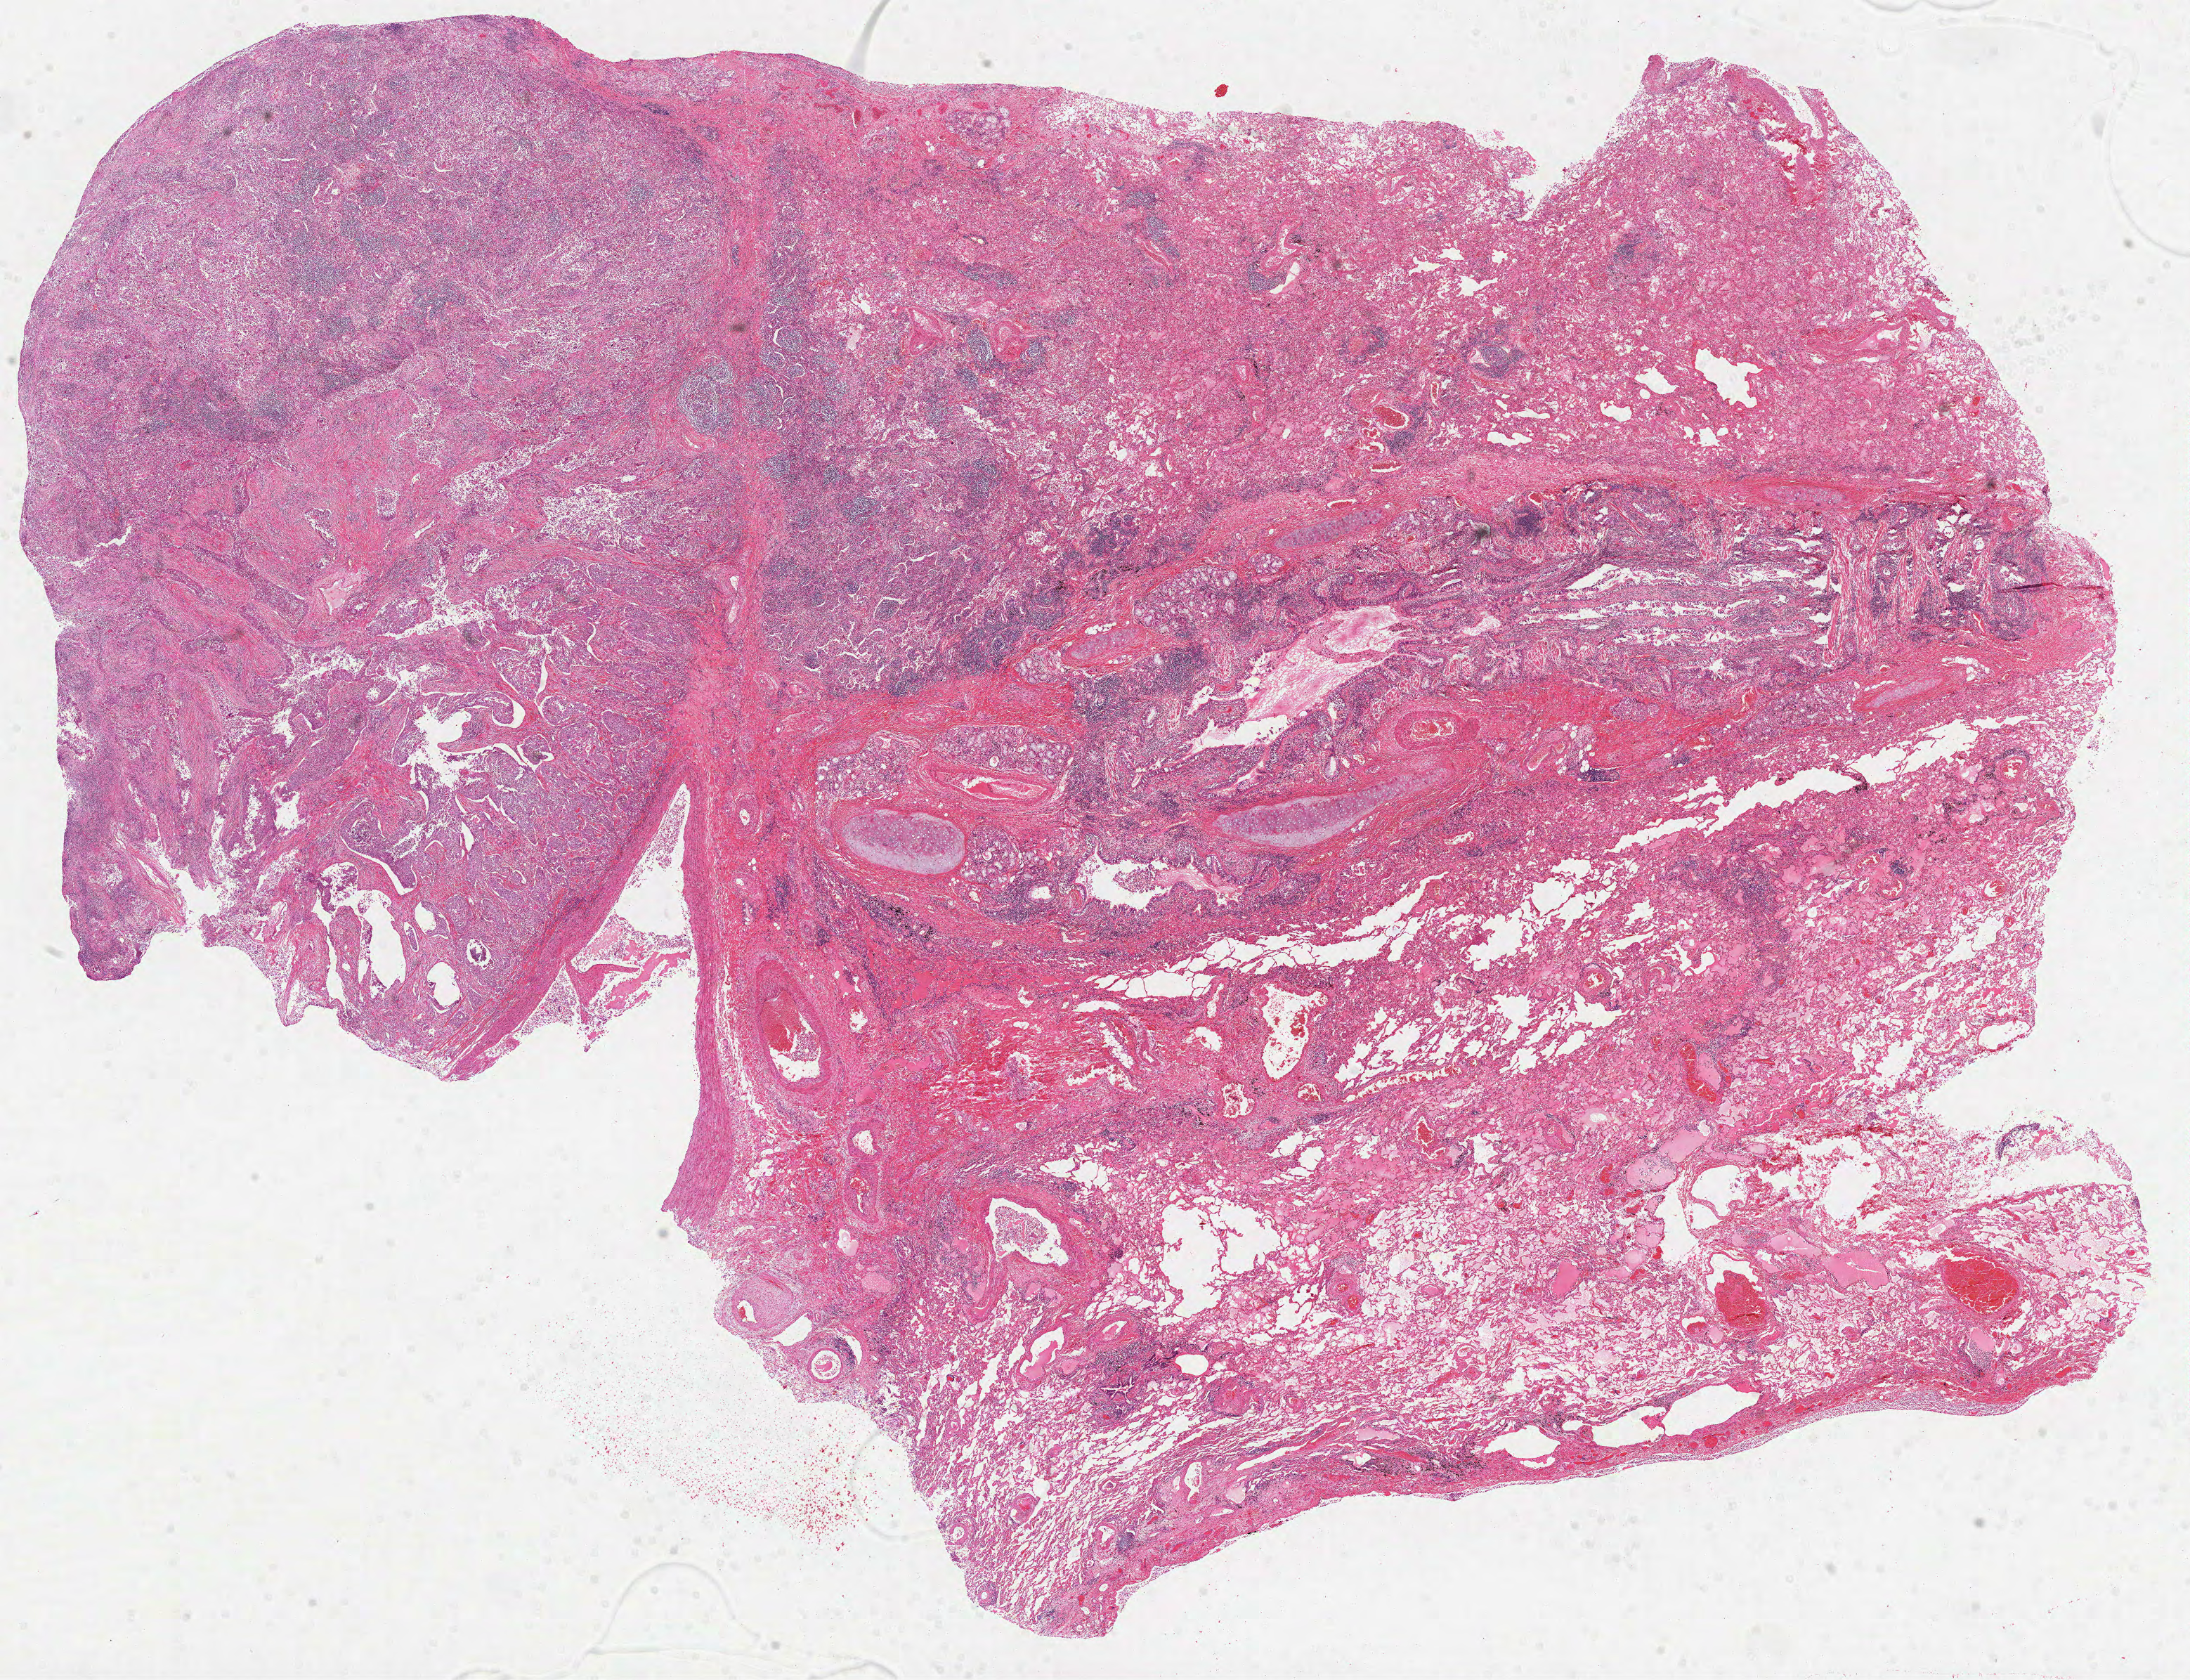
Whole-slide histology image, H&E-stained — shown as a low-resolution overview of the whole scanned area (about 25.1 x 19.3 mm, from a 40x scan); formalin-fixed paraffin-embedded (FFPE) diagnostic section; sample: primary tumour, lung. Male patient; age at initial diagnosis 65 years.
• AJCC pathologic stage: IIB (6th edition)
• laterality: left
• pathologic diagnosis: Squamous cell carcinoma, NOS